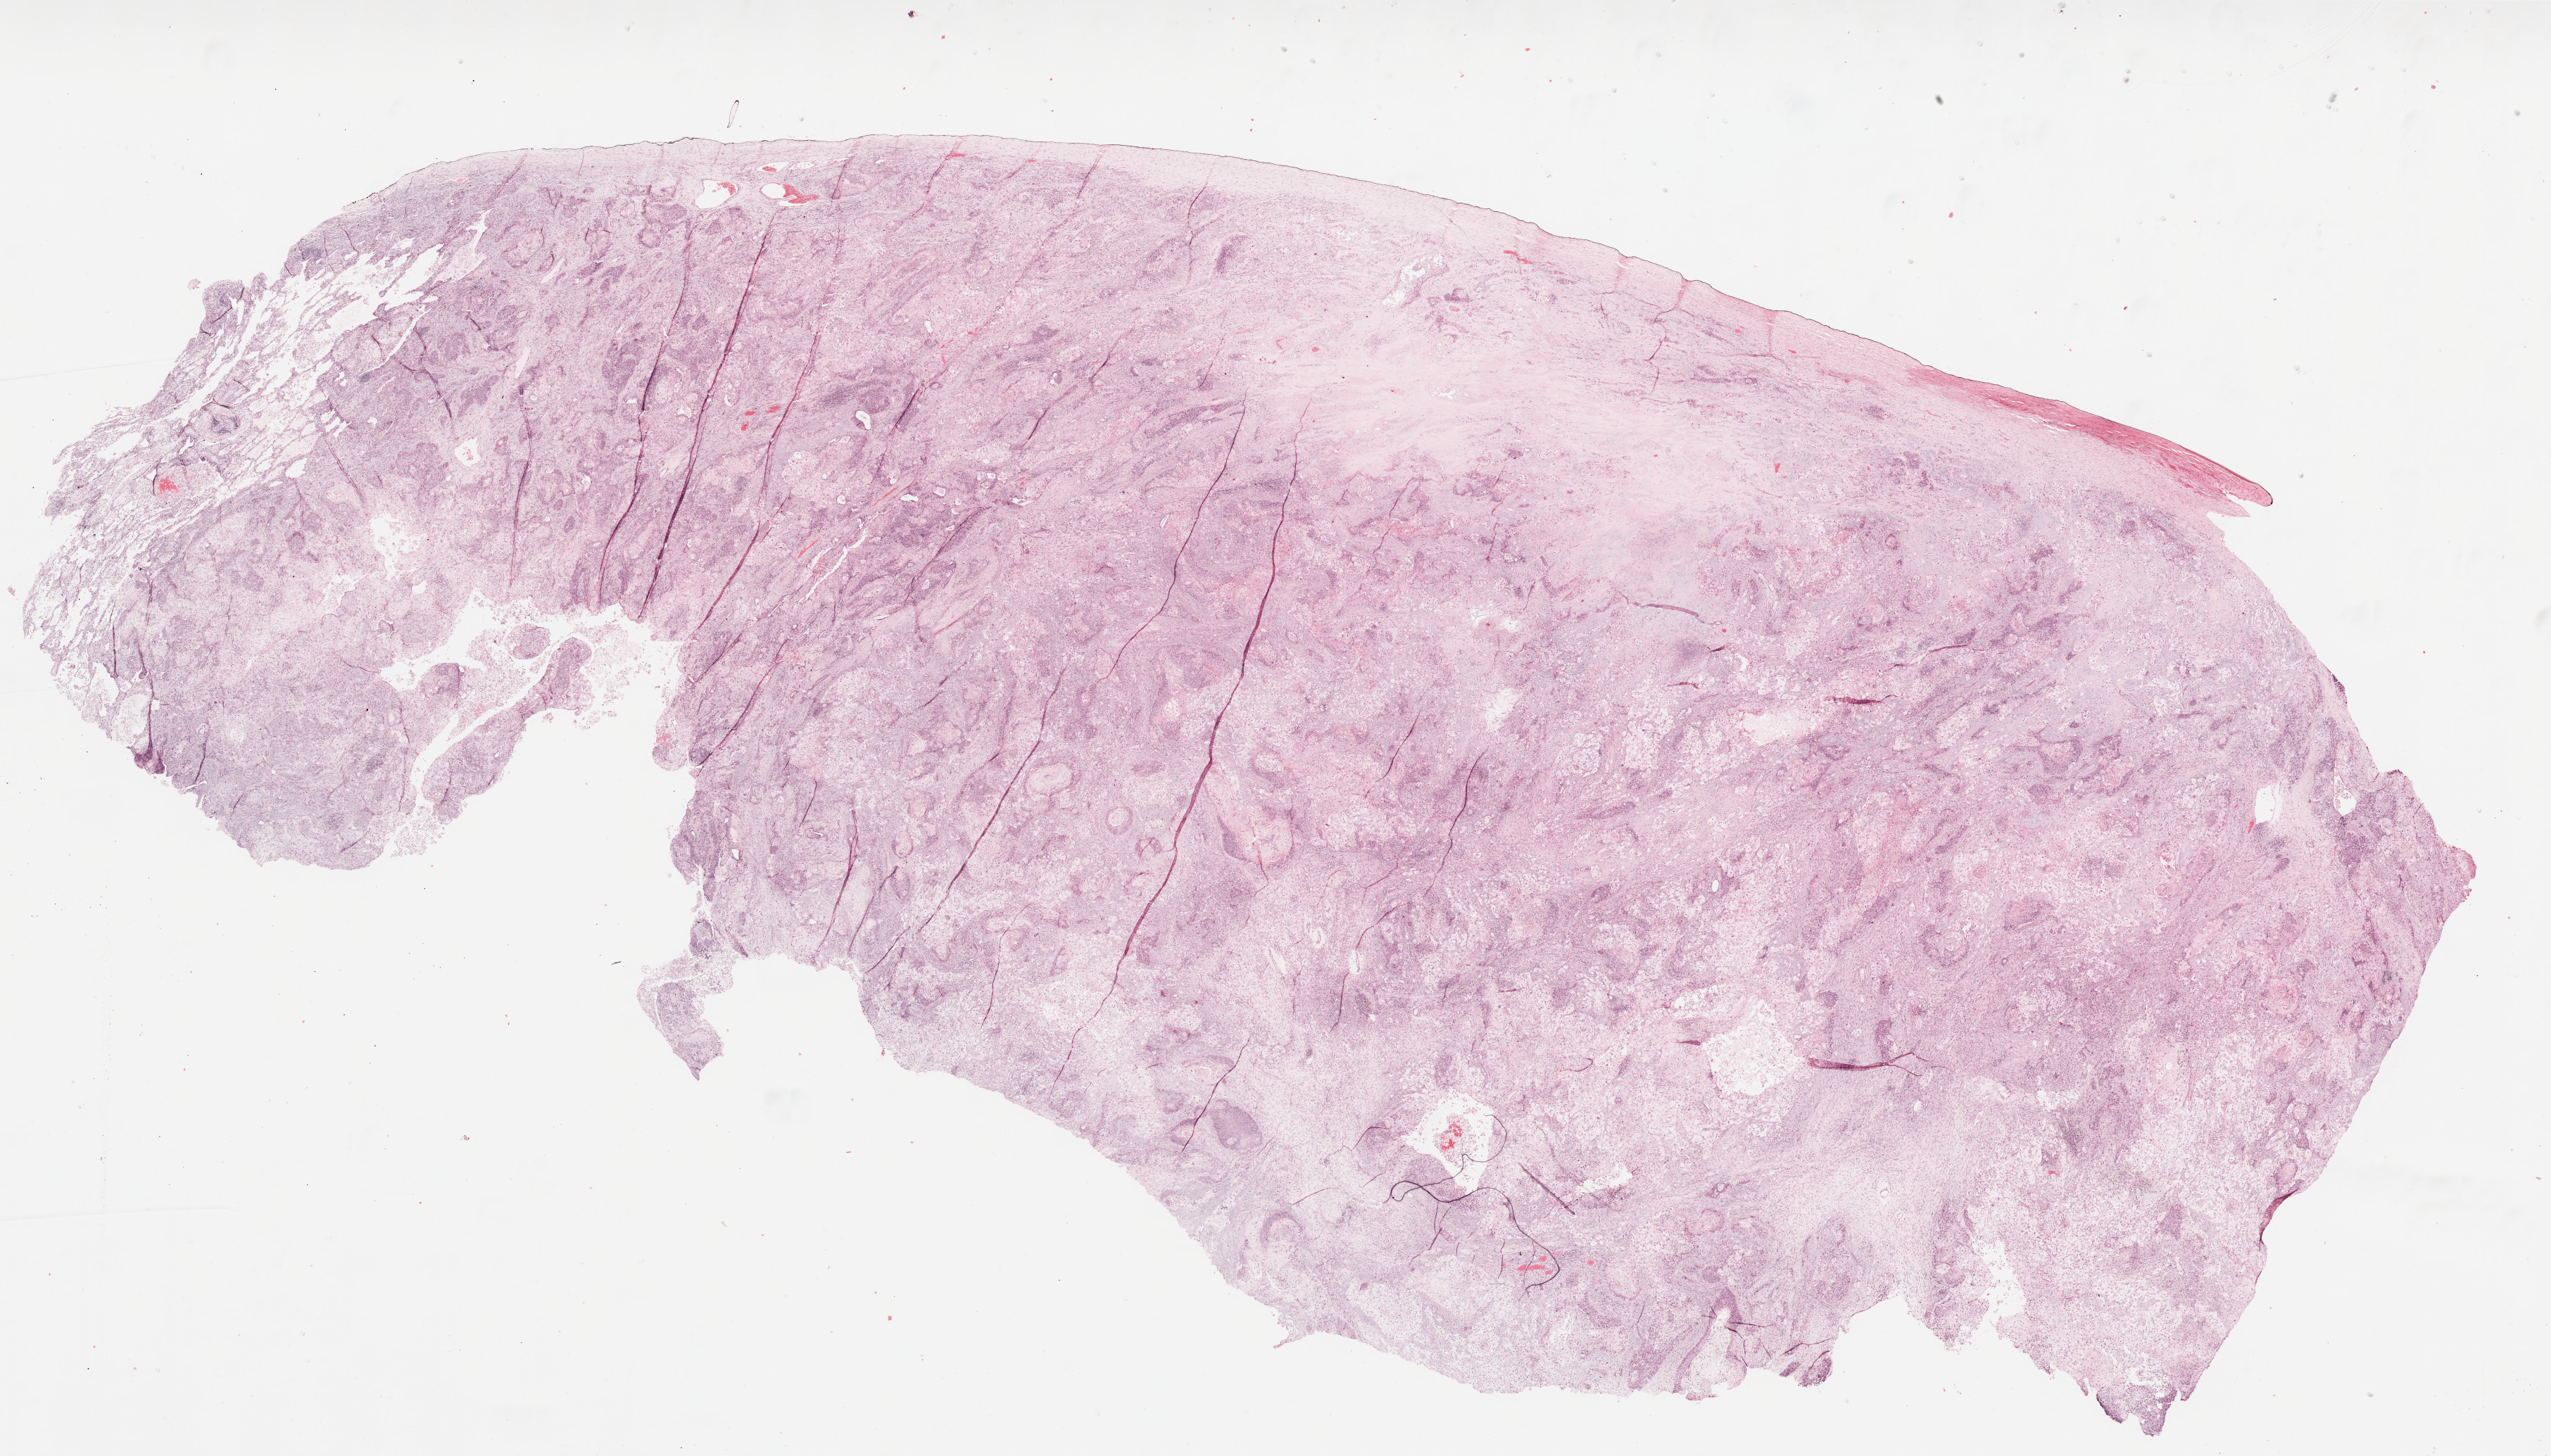
Hematoxylin and eosin (H&E) stained whole-slide image — a low-resolution overview of the entire scanned area, about 29.1 x 16.6 mm (from a 20x scan); formalin-fixed paraffin-embedded (FFPE) diagnostic section; primary tumour sample from the lung. Female patient; age at initial diagnosis 64 years.
AJCC pathologic stage: IIB. TNM: T2 N1 M0. Pathologic diagnosis: Squamous cell carcinoma, NOS (lower lobe, lung).